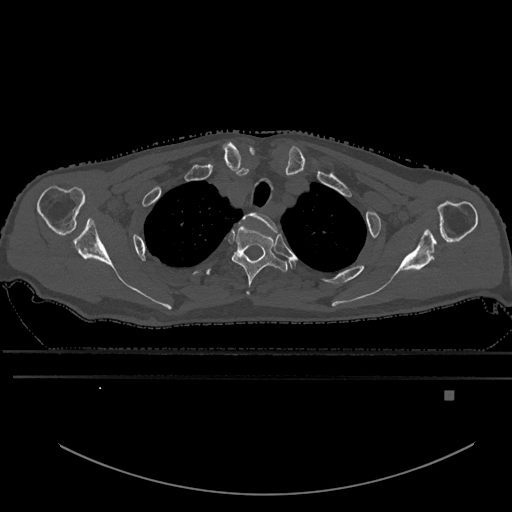
CT including the spine, one axial slice. Position 496 of 969 along the scan axis. Bone window (W 1800 / L 400 HU). 0.5 mm slice thickness. 512 × 512 image matrix, field of view 456 × 456 mm. Patient: male, 82 years. From the clinical record (not read from this slice): primary cancer: prostate.
Structures marked on this image (semi-automatically segmented with operator editing):
- T1 vertebra: bounding box <244,212,278,232> (left, top, right, bottom; pixels)
- T2 vertebra: <231,224,288,295>